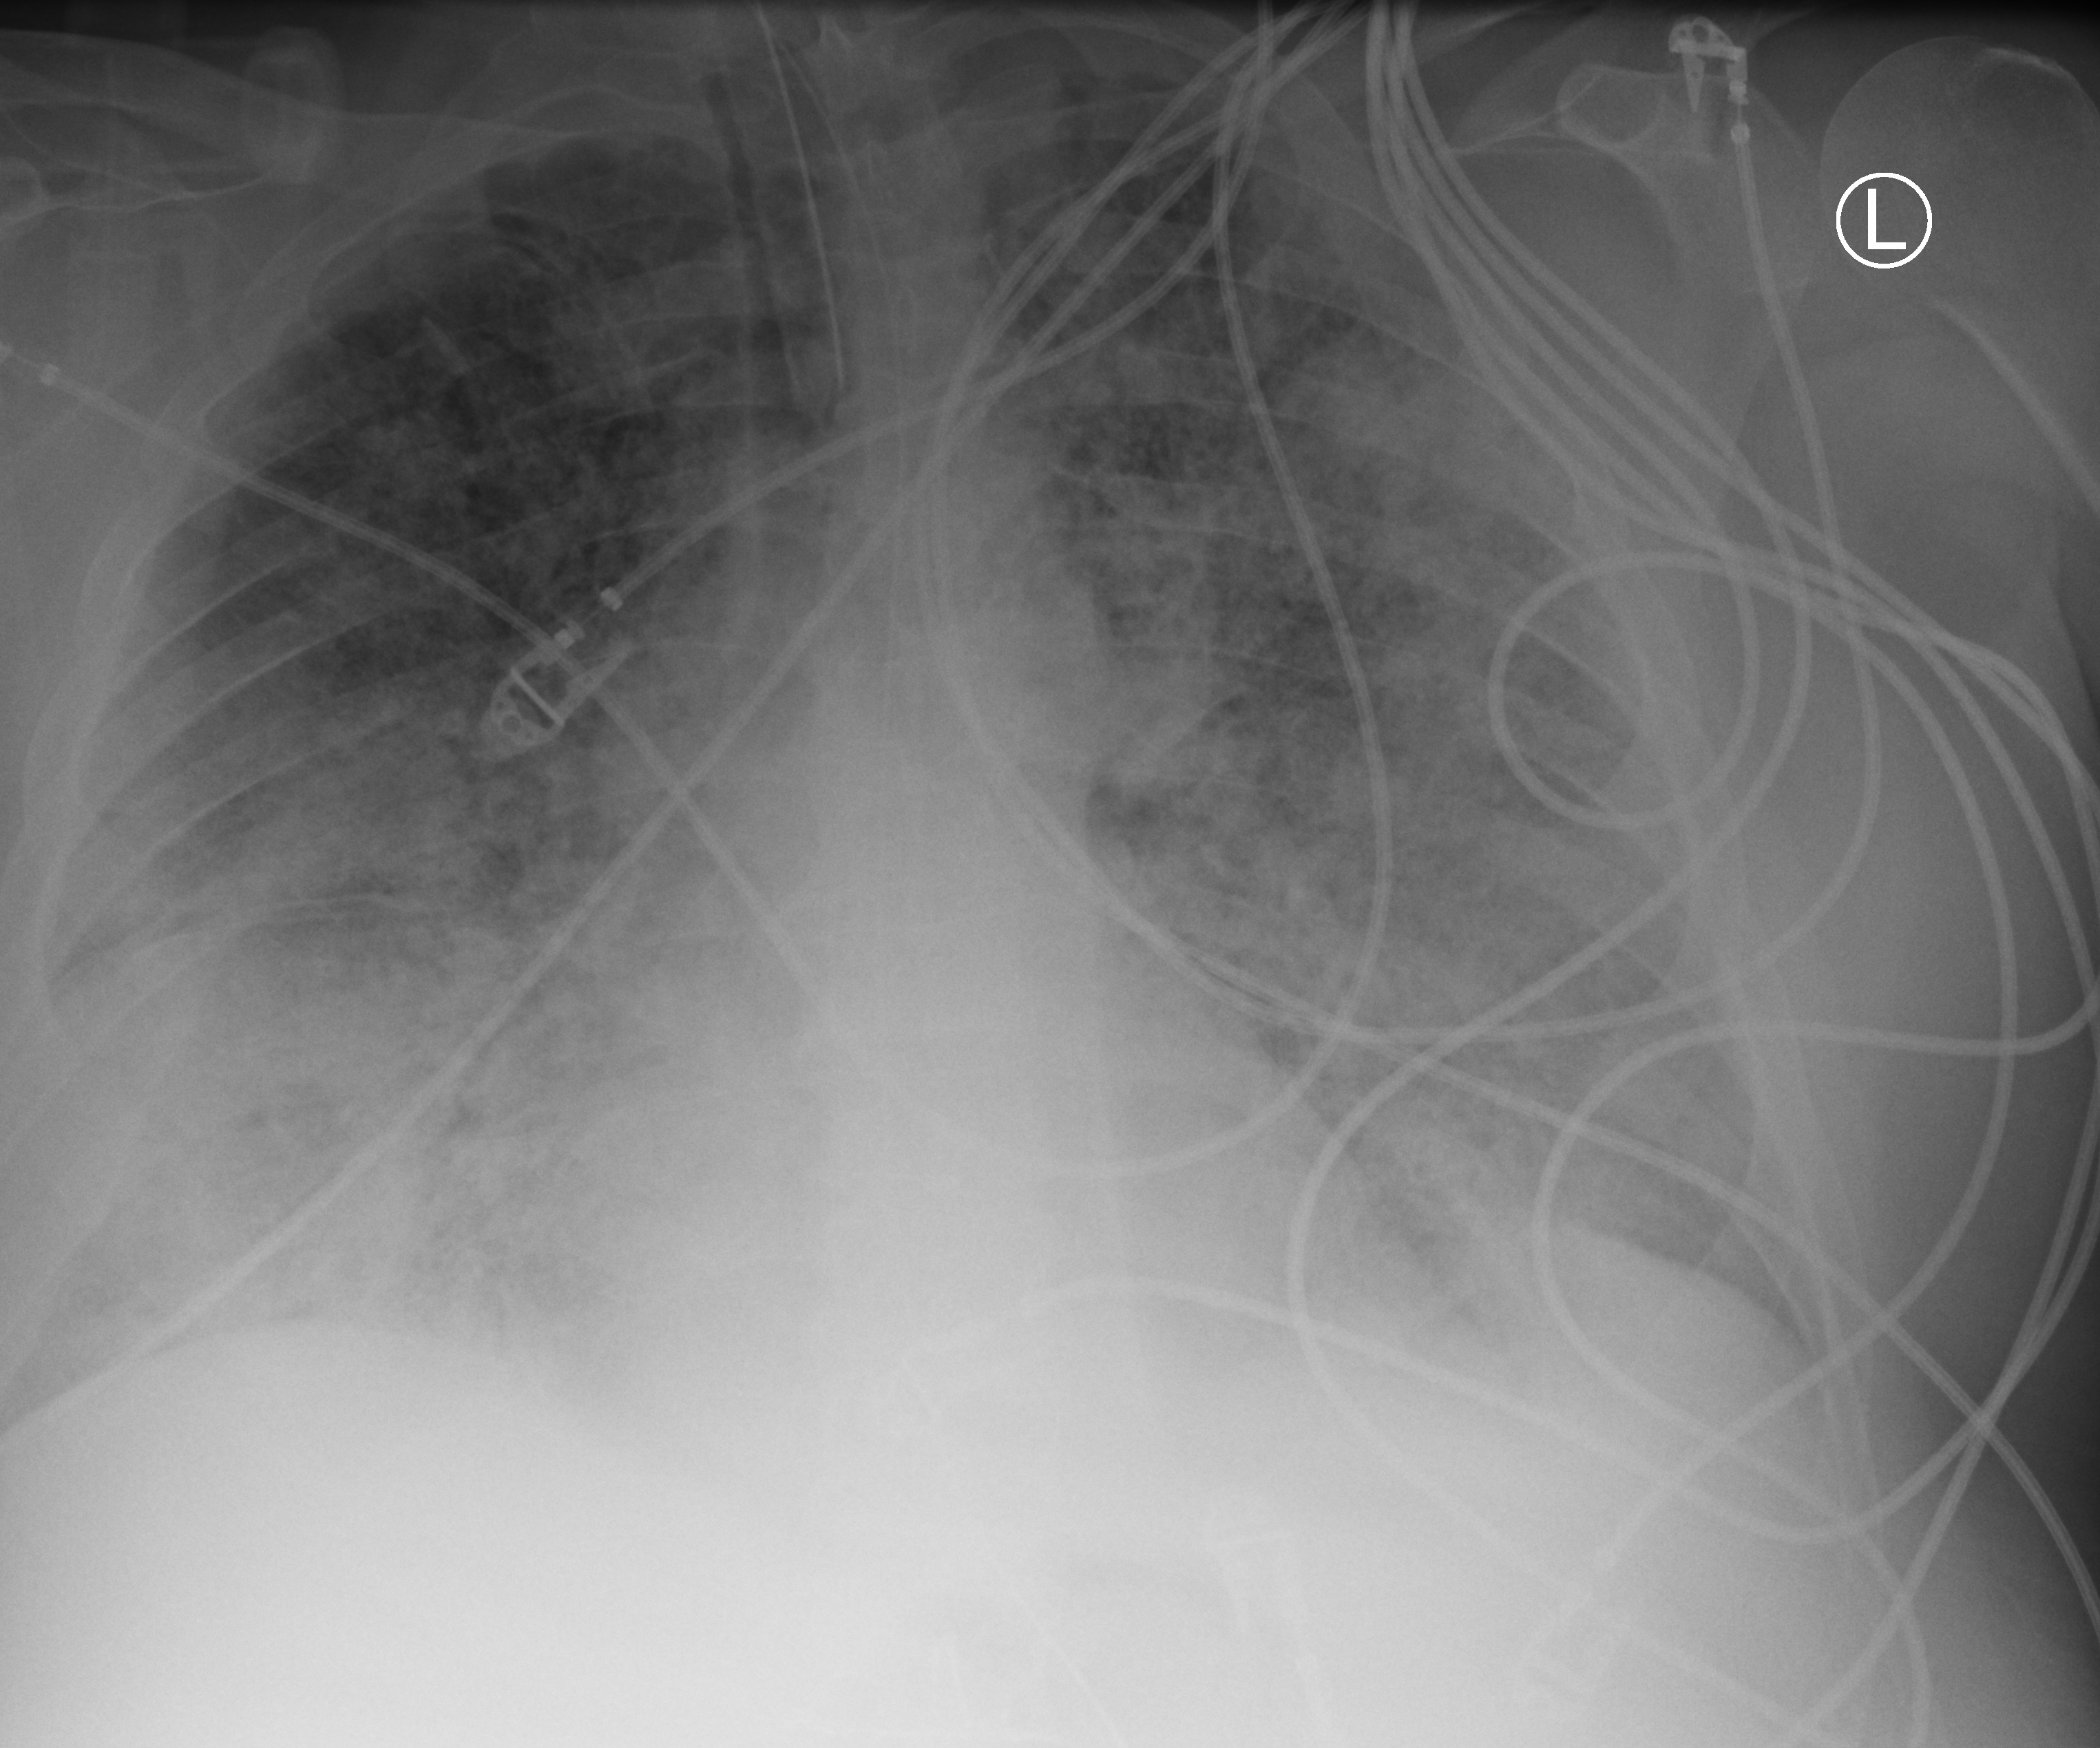
Bedside chest radiograph (computed radiography), anteroposterior (AP) projection. Male patient hospitalised with COVID-19, age 60–74 years.
From the hospital-stay record, not from the radiograph (when in the stay this image was taken is not recorded): chronic kidney disease (admission record): no.